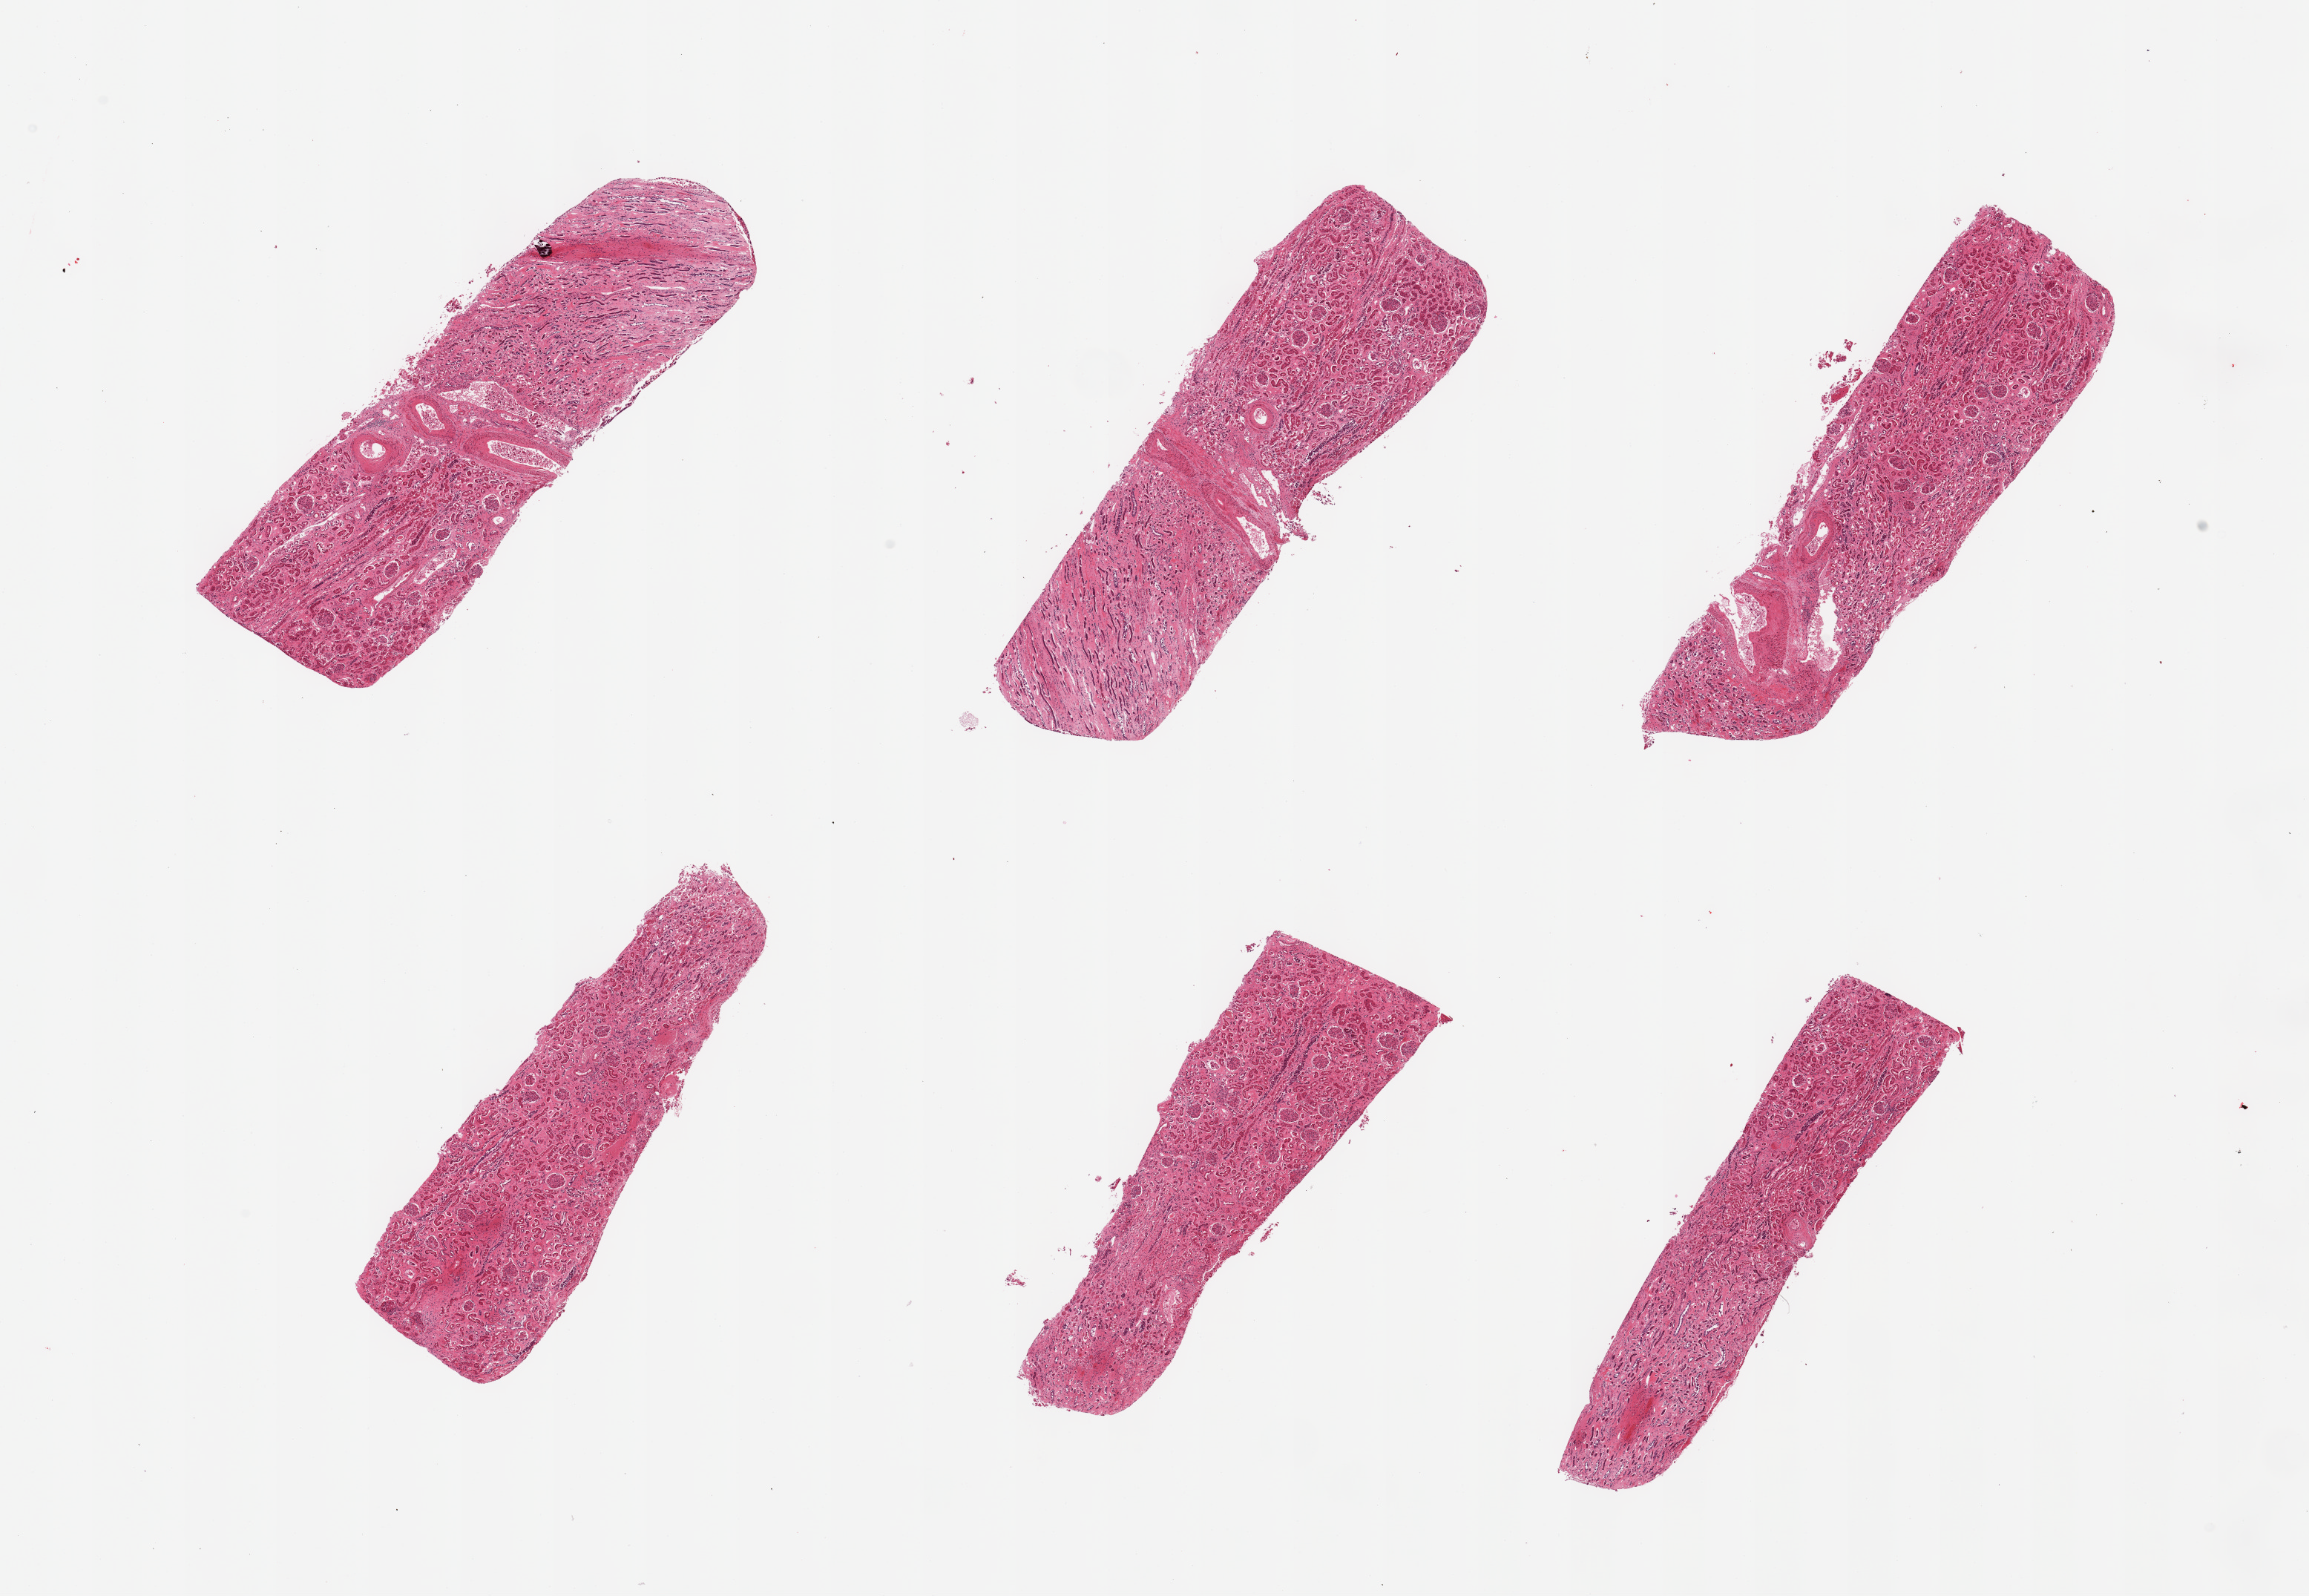
H&E whole-slide image, low-resolution overview of the scanned area, about 24.6 x 17.0 mm, PAXgene-fixed, paraffin-embedded tissue, sampled site (target tissue): renal cortex, tissue donor sample. Donor sex: male.
Pathologist's review note for this sample: 6 pieces; renal cortex (target) and medulla (not target), arteriosclerosis.